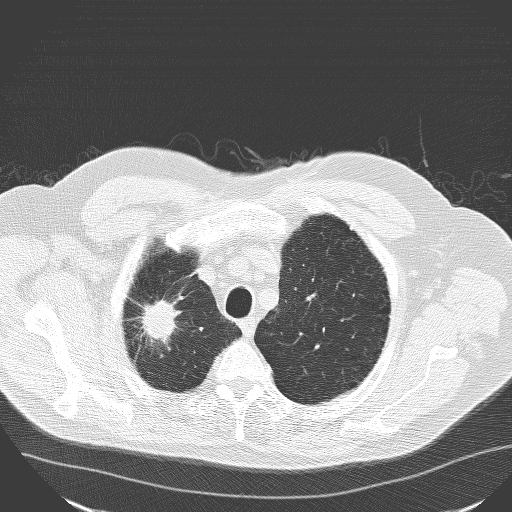
Chest CT (low-dose screening protocol), one axial image, first (baseline) screen, lung window (W 1500 / L -600 HU), lung (sharp) reconstruction kernel (D), slice 137 of 160 in the series, 512 × 512 image matrix, field of view 400 × 400 mm. Male participant, aged 71 years at enrolment. Current smoker at enrolment.
Expert reader's lesion annotation, bounding box [x1, y1, x2, y2] px = [117, 283, 189, 358]. Screening reader's record for this exam (one nodule recorded; not confirmed to be the boxed lesion): non-calcified nodule or mass ≥4 mm, right upper lobe, 30 × 25 mm, spiculated (stellate) margins, soft tissue attenuation. Lung cancer was diagnosed 182 days after this screen: squamous cell carcinoma, NOS, right upper lobe, poorly differentiated (G3), stage IA (AJCC 6th edition), 30 mm at pathology.